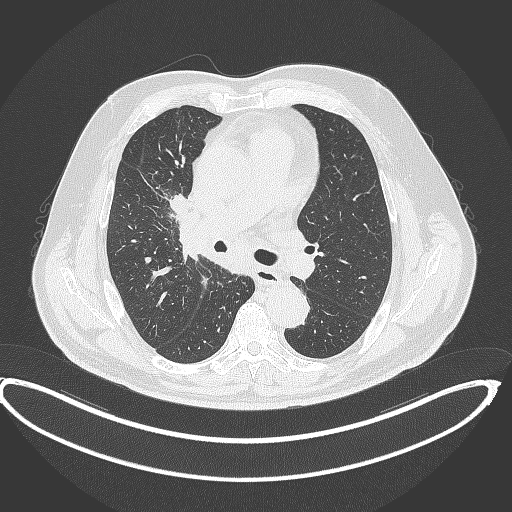
Chest CT, one axial slice; slice 245 of 390 in the series (ordered by position); lung window (W 1500 / L -600 HU); 1 mm slice thickness; 512 × 512 image matrix. Male patient, age 62 years. From the clinical record (not read from this slice): clinical TNM (as recorded): T1c N3 M1c.
Outlined on this slice (bounding box drawn by a radiologist):
- lung tumour (recorded histology: adenocarcinoma): box from (x=165, y=189) to (x=192, y=213) px